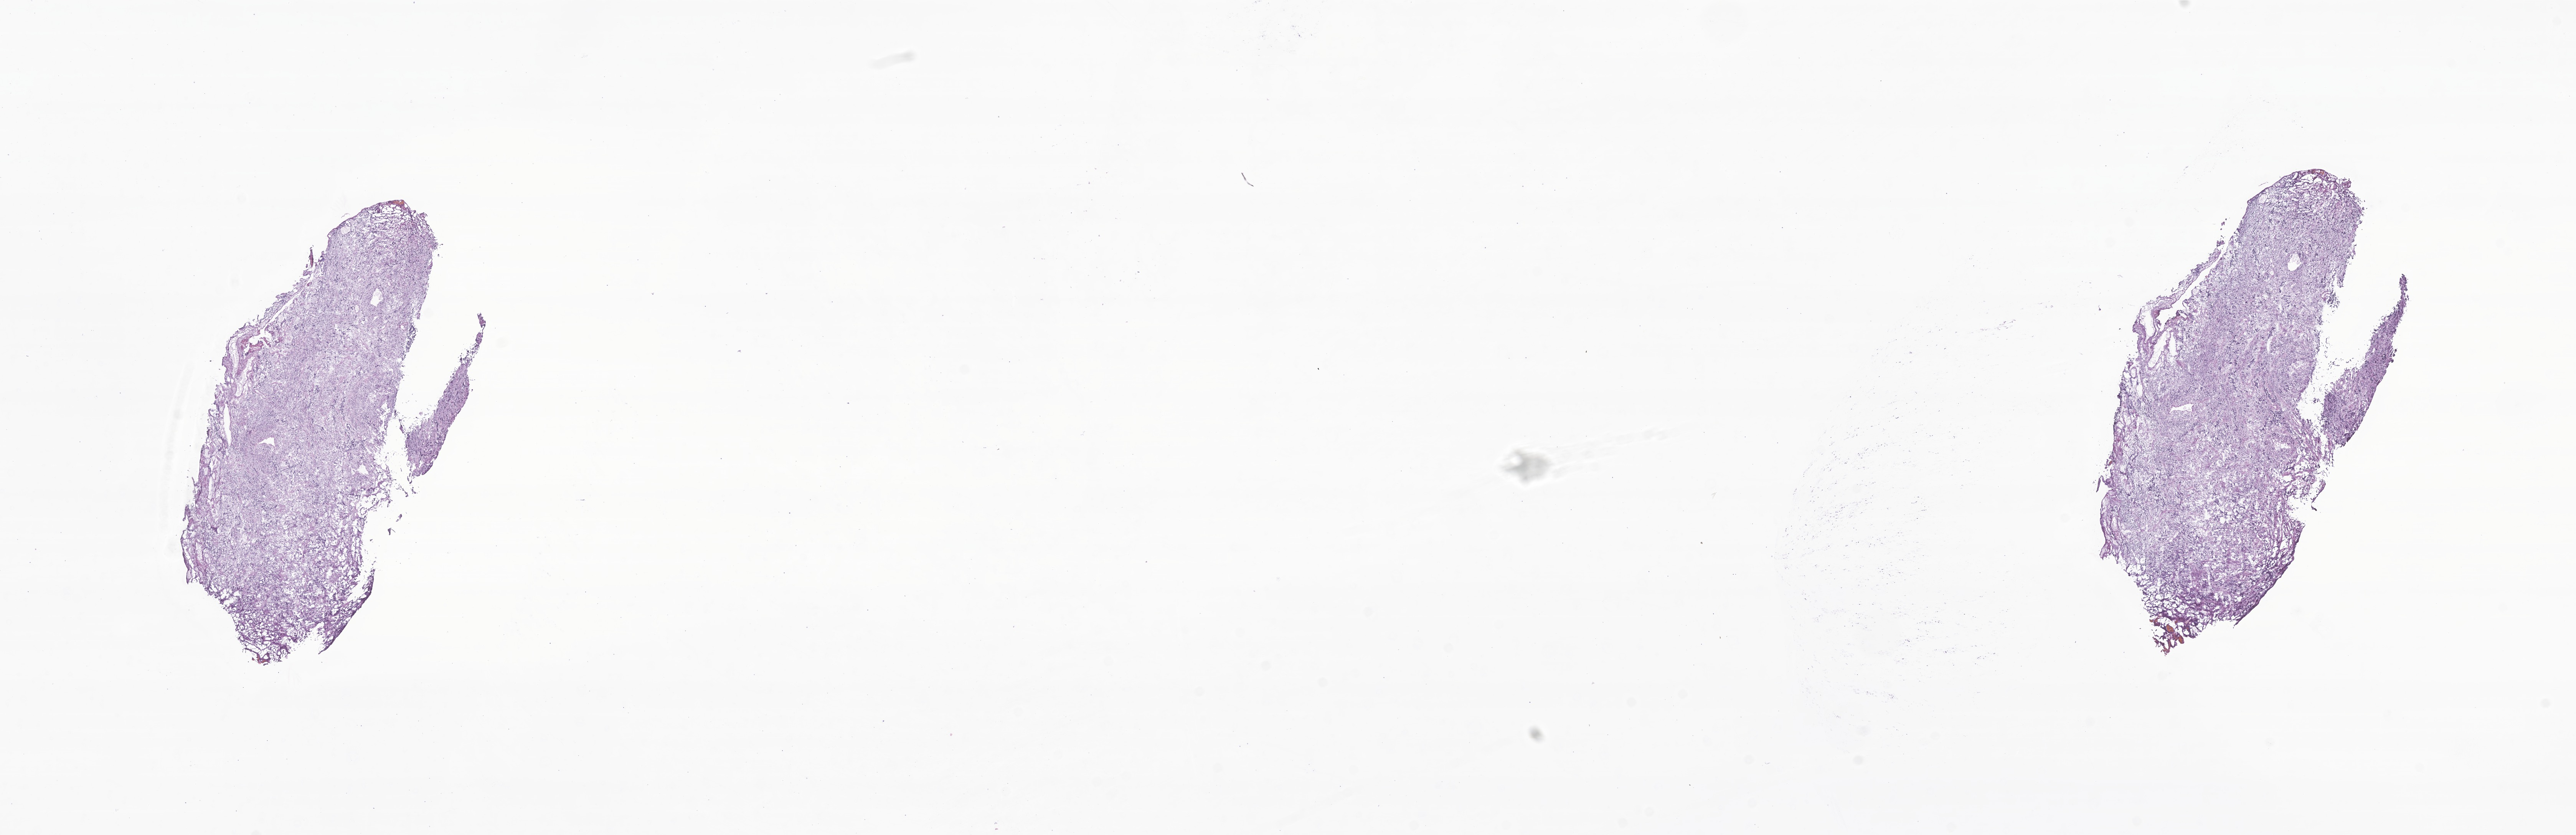
Haematoxylin and eosin whole-slide image of tumor tissue from the cerebellum — low-resolution overview of the scanned area, about 28.3 x 9.2 mm, frozen section. Patient male; age 105 months.
Diagnosis: Medulloblastoma, NOS.